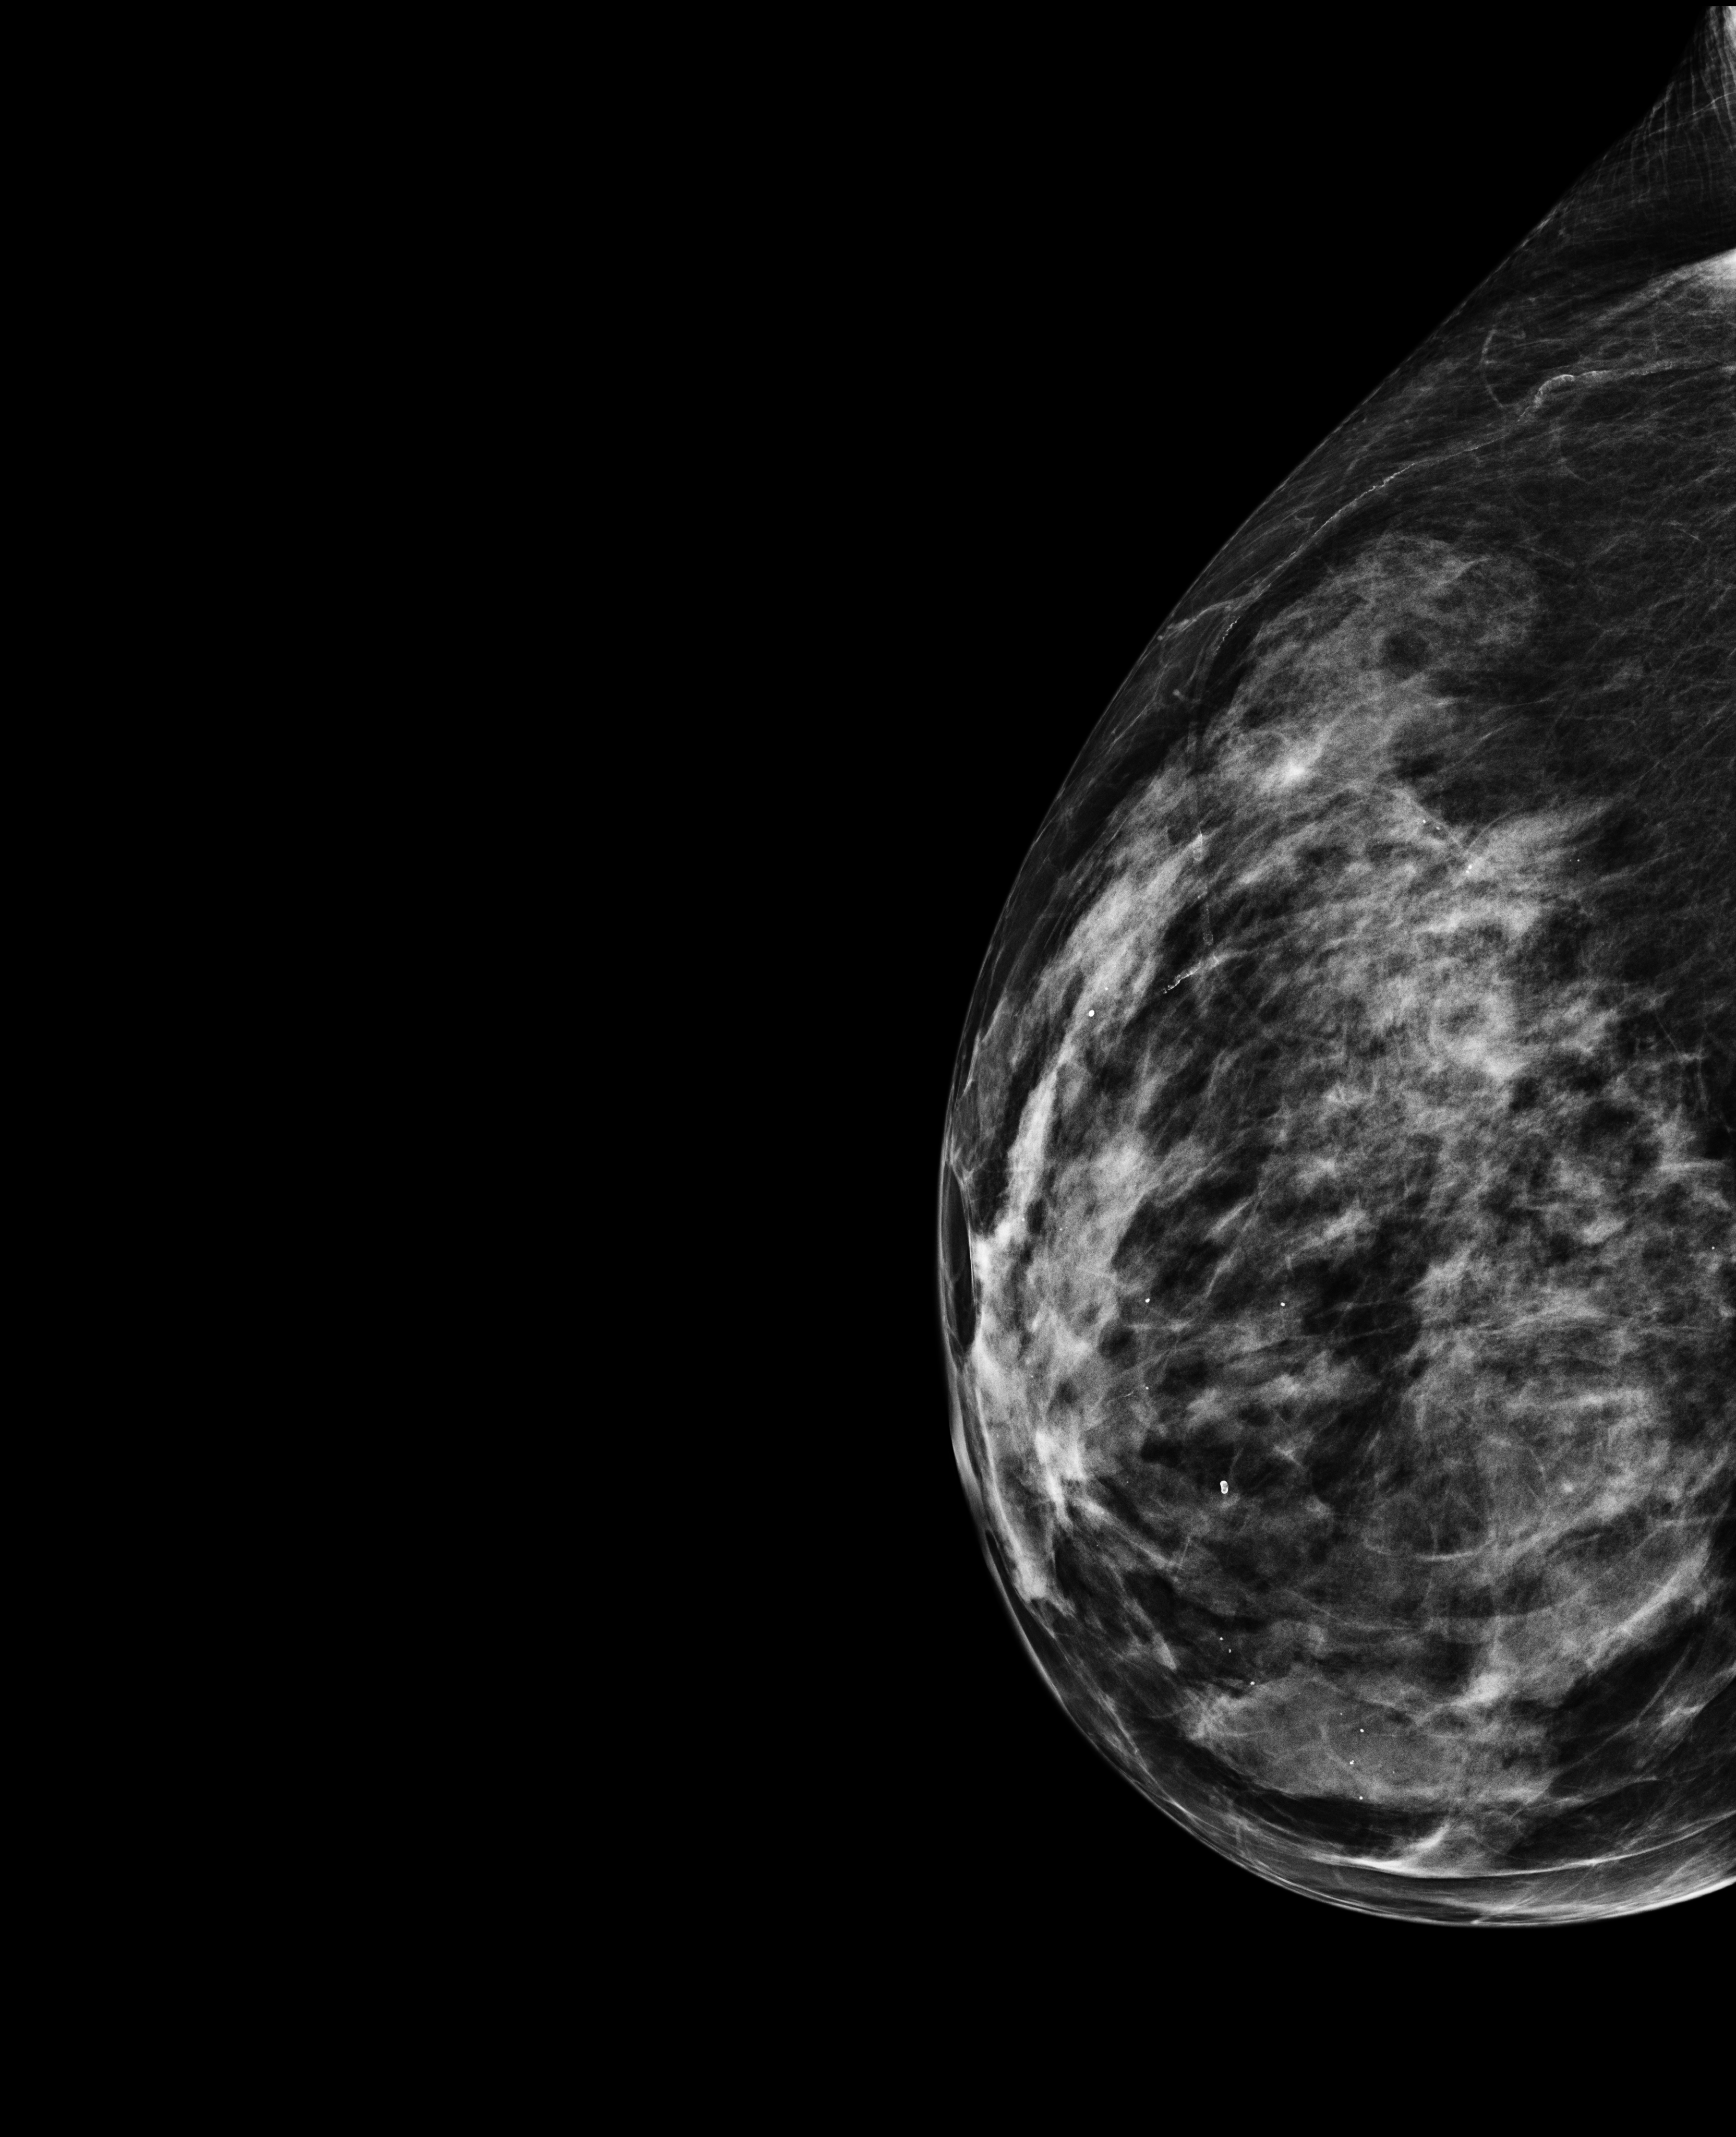
Screening examination. Patient aged 75 years (female).
Image type: full-field digital mammogram. Breast: right. Projection: laterally exaggerated craniocaudal (XCCL) view.